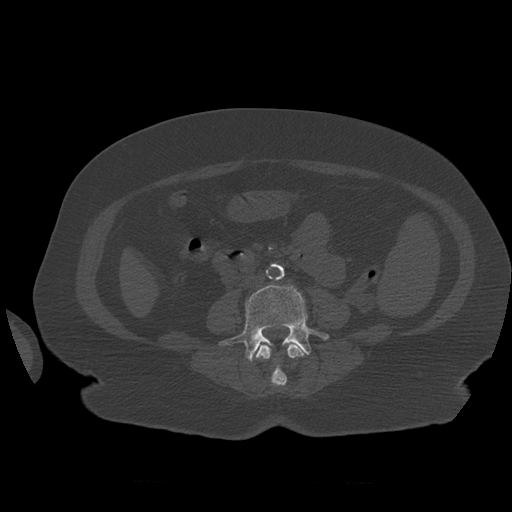
CT including the spine, one axial slice; position 213 of 399 along the scan axis; reconstruction kernel STANDARD; 120 kVp; bone window (W 1800 / L 400 HU); 1.25 mm slice thickness; 512 × 512 image matrix, field of view 404 × 404 mm. Patient age 81 years. Case-level facts recorded for this patient, not image findings: primary cancer: renal; vertebrae with lytic lesions (as recorded): L1.
Outlined on this slice (semi-automatically segmented with operator editing):
- L3 vertebra: box from (x=256, y=343) to (x=307, y=386) px
- L4 vertebra: (x=219, y=284)–(x=329, y=362)